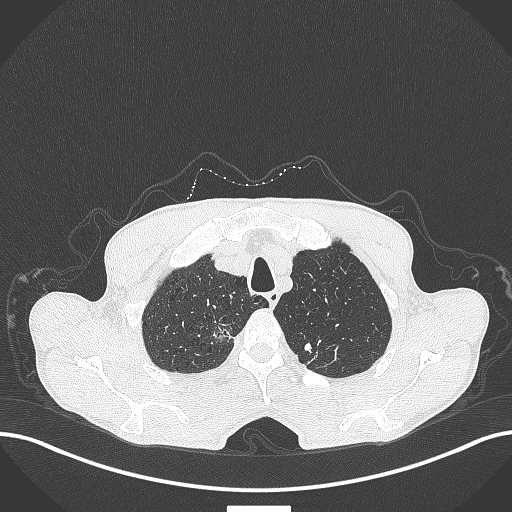
Chest CT, one axial slice; position 372 of 445 along the scan axis; 120 kVp; lung window (W 1500 / L -600 HU); 512 × 512 image matrix, field of view 400 × 400 mm. Patient: male, 70 years. From the clinical record (not read from this slice): clinical TNM (as recorded): T1a N0 M0.
Outlined on this slice (bounding box drawn by a radiologist):
- lung tumour (recorded histology: adenocarcinoma): bounding box [x1, y1, x2, y2] px = [208, 314, 239, 347]